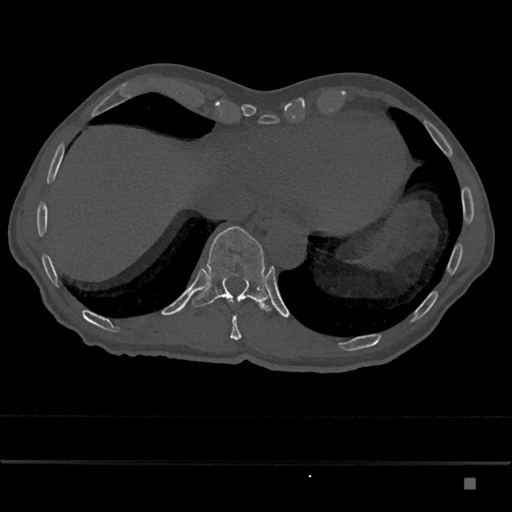
CT including the spine, one axial slice; position 698 of 797 along the scan axis; bone window (W 1800 / L 400 HU); 512 × 512 image matrix, field of view 390 × 390 mm. Patient: male, 72 years. Case-level facts recorded for this patient, not image findings: primary cancer: prostate.
Outlined on this slice (semi-automatic segmentation, software-assisted and operator-edited):
- T10 vertebra: bounding box (x1, y1, x2, y2) in pixels: (229, 299, 242, 340)
- T11 vertebra: (192, 226, 272, 312)